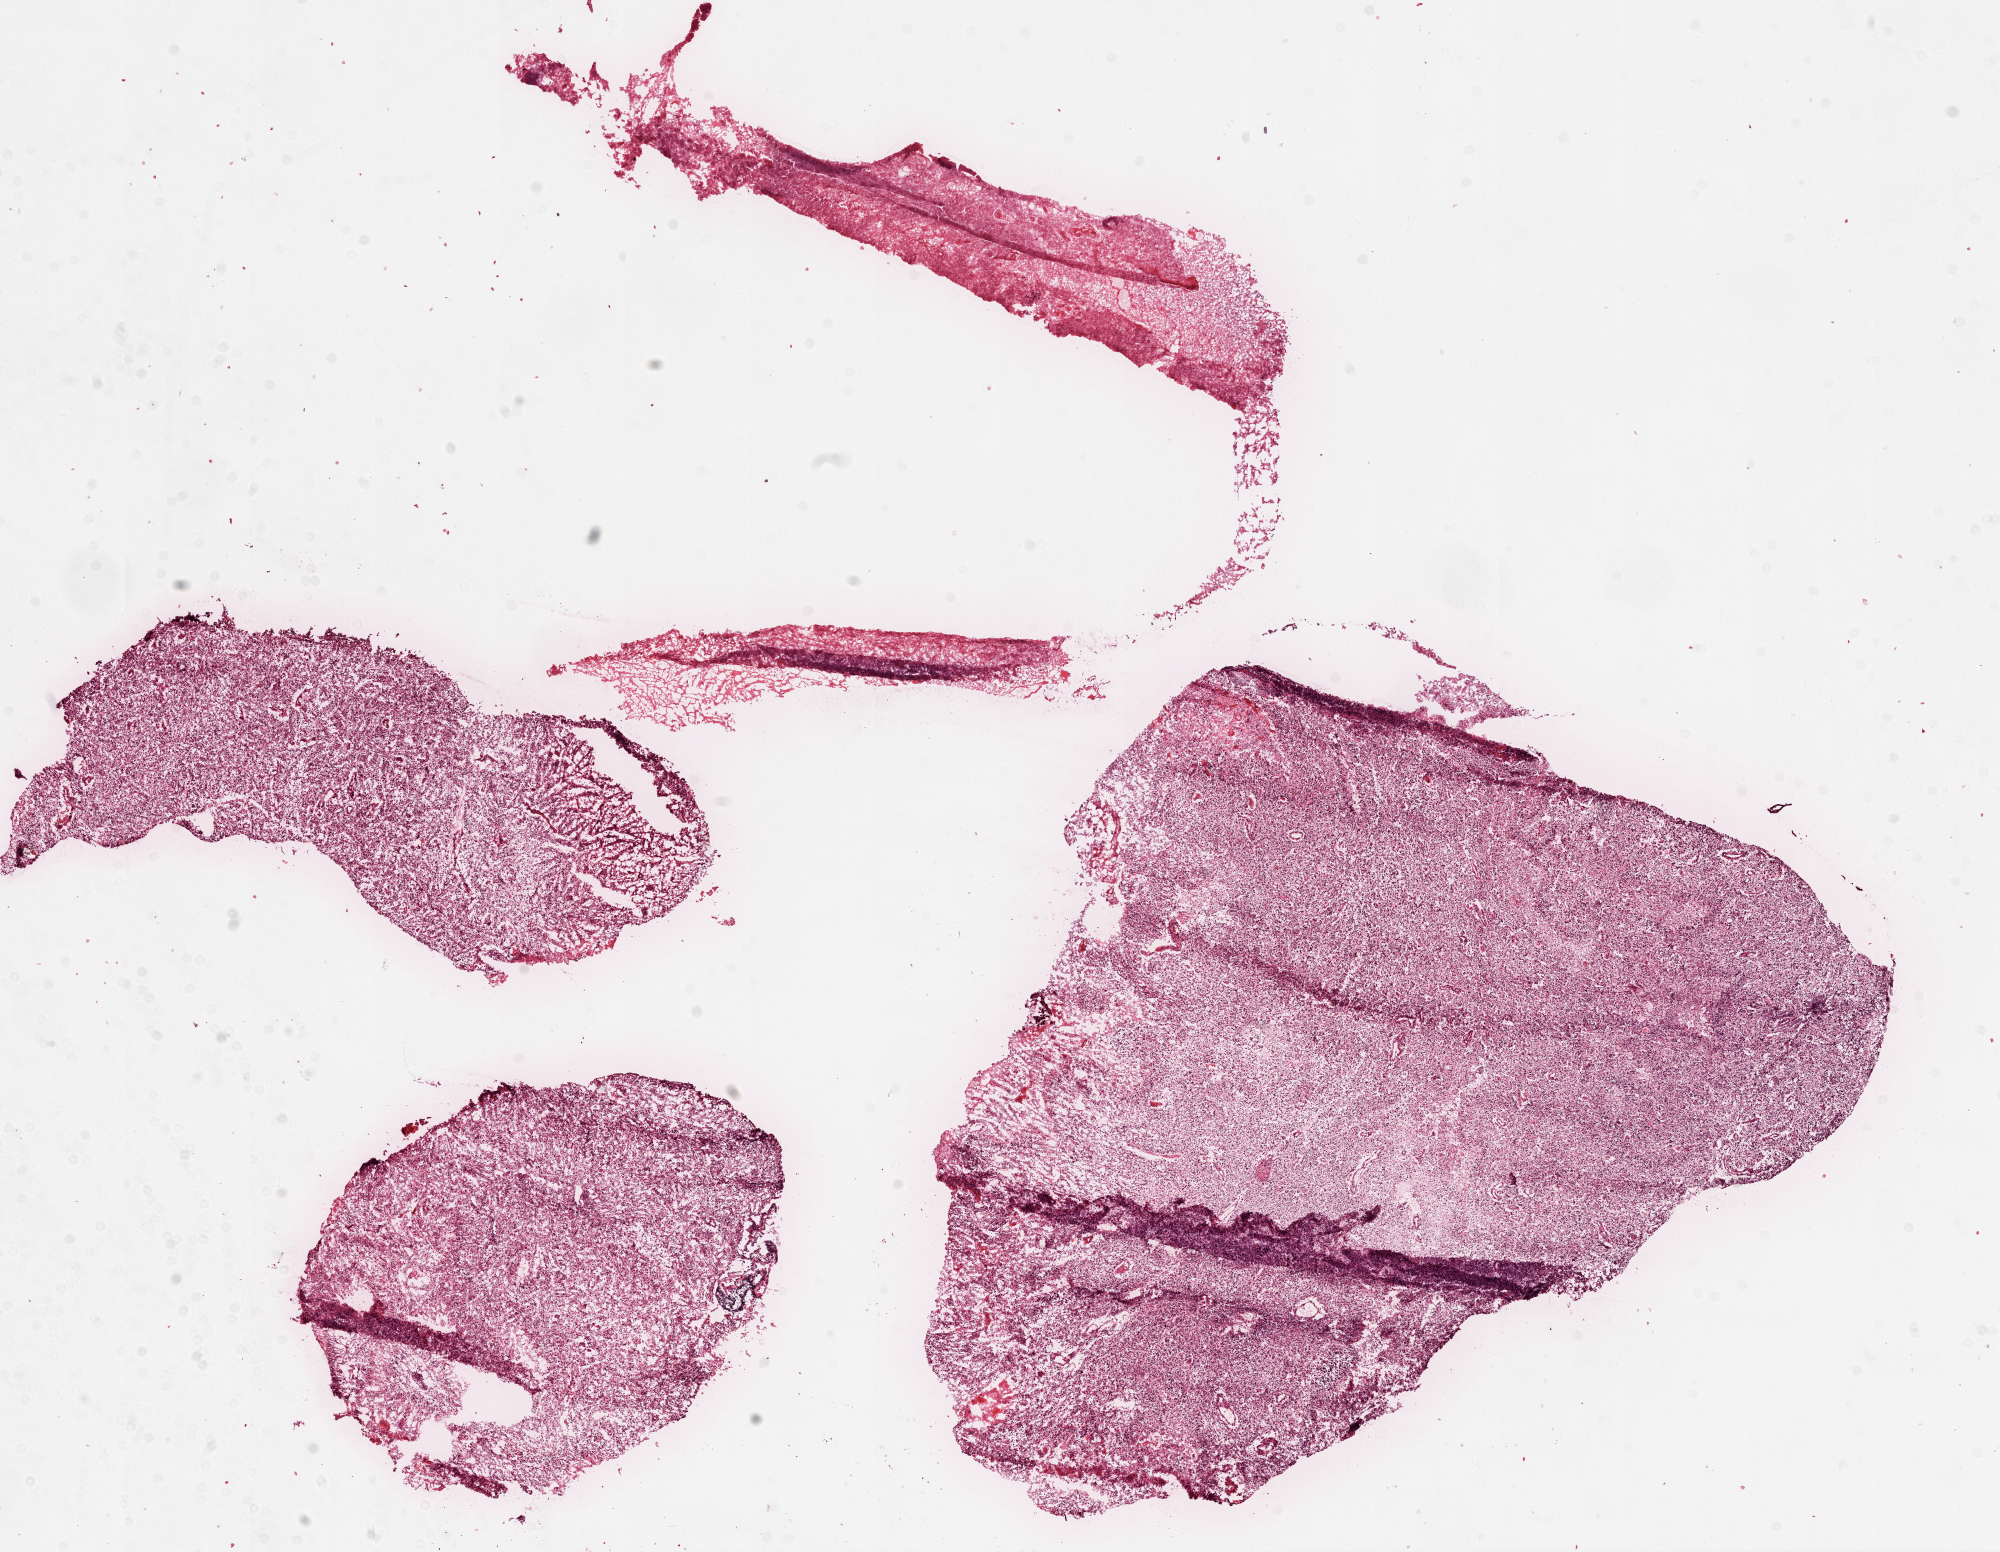
Whole-slide histology image, H&E — shown as a low-resolution overview of the whole scanned area (about 16.0 x 12.5 mm, acquisition: 20x scan). Frozen section from the top of the tissue portion. Brain, primary tumour sample. Male patient; age at initial diagnosis 60 years. Slide review estimates, as recorded: tumour cells 90%, tumour nuclei 100%, normal cells 0%, stromal cells 0%, necrosis 10%.
Histologic diagnosis: Glioblastoma.